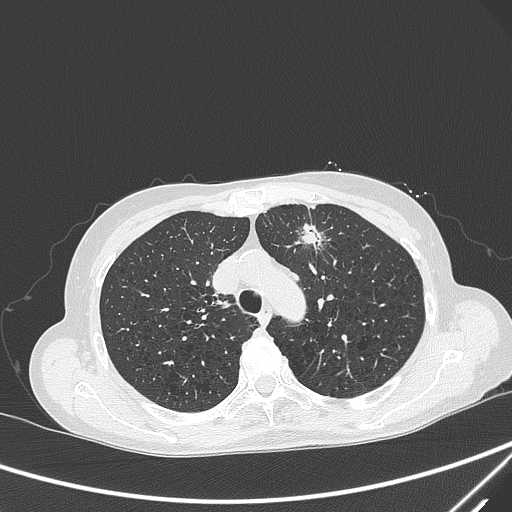
Chest CT, one axial slice; position 225 of 299 along the scan axis; 120 kVp; lung window (W 1500 / L -600 HU); 1 mm slice thickness; 512 × 512 image matrix, field of view 350 × 350 mm. Female patient, age 71 years. Case-level facts recorded for this patient, not image findings: clinical TNM (as recorded): T1c N0 M0; histopathological grade: G2-3.
Annotated regions visible in this slice (bounding box drawn by a radiologist):
- lung tumour (recorded histology: adenocarcinoma): bounding box <293,216,326,257> (left, top, right, bottom; pixels)